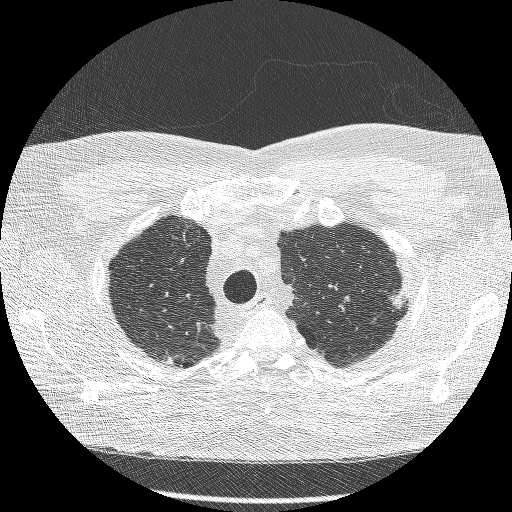
Chest CT (low-dose screening protocol), one axial image; second annual screen; lung window (W 1500 / L -600 HU); 1.25 mm slice thickness; lung (sharp) reconstruction kernel (BONE); 512 × 512 image matrix. Male participant, aged 66 years at enrolment. Current smoker at enrolment.
Expert-annotated lung lesion, bounding box <382,275,420,322> (left, top, right, bottom; pixels). Reader record for this screening exam (exam-level; its link to the box is not recorded): non-calcified nodule or mass ≥4 mm, right lower lobe, 40 × 19 mm, spiculated (stellate) margins, soft tissue attenuation, pre-existing on the prior screen: yes; interval growth: no. Note: the box lies in the patient's left hemithorax on this image, whereas the reader's record names the right lung; they may be different findings. Participant outcome: lung cancer diagnosed 554 days after this screen (after the third annual screen) — adenocarcinoma, NOS, left upper lobe, poorly differentiated (G3), stage IB (AJCC 6th edition), 16 mm at pathology.